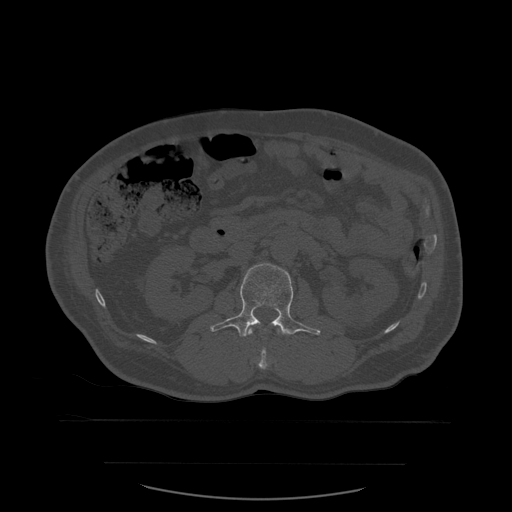
CT including the spine, one axial slice. Slice 224 of 590 in the series (ordered by position). Bone window (W 1800 / L 400 HU). 1.25 mm slice thickness. 512 × 512 image matrix, field of view 479 × 479 mm. Patient age 71 years. From the clinical record (not read from this slice): primary cancer: lung; vertebrae with lytic lesions (as recorded): T1, T2, L5, S1.
Annotated regions visible in this slice (semi-automatically segmented with operator editing):
- L1 vertebra: bounding box <249,330,279,370> (left, top, right, bottom; pixels)
- L2 vertebra: <210,264,321,337>